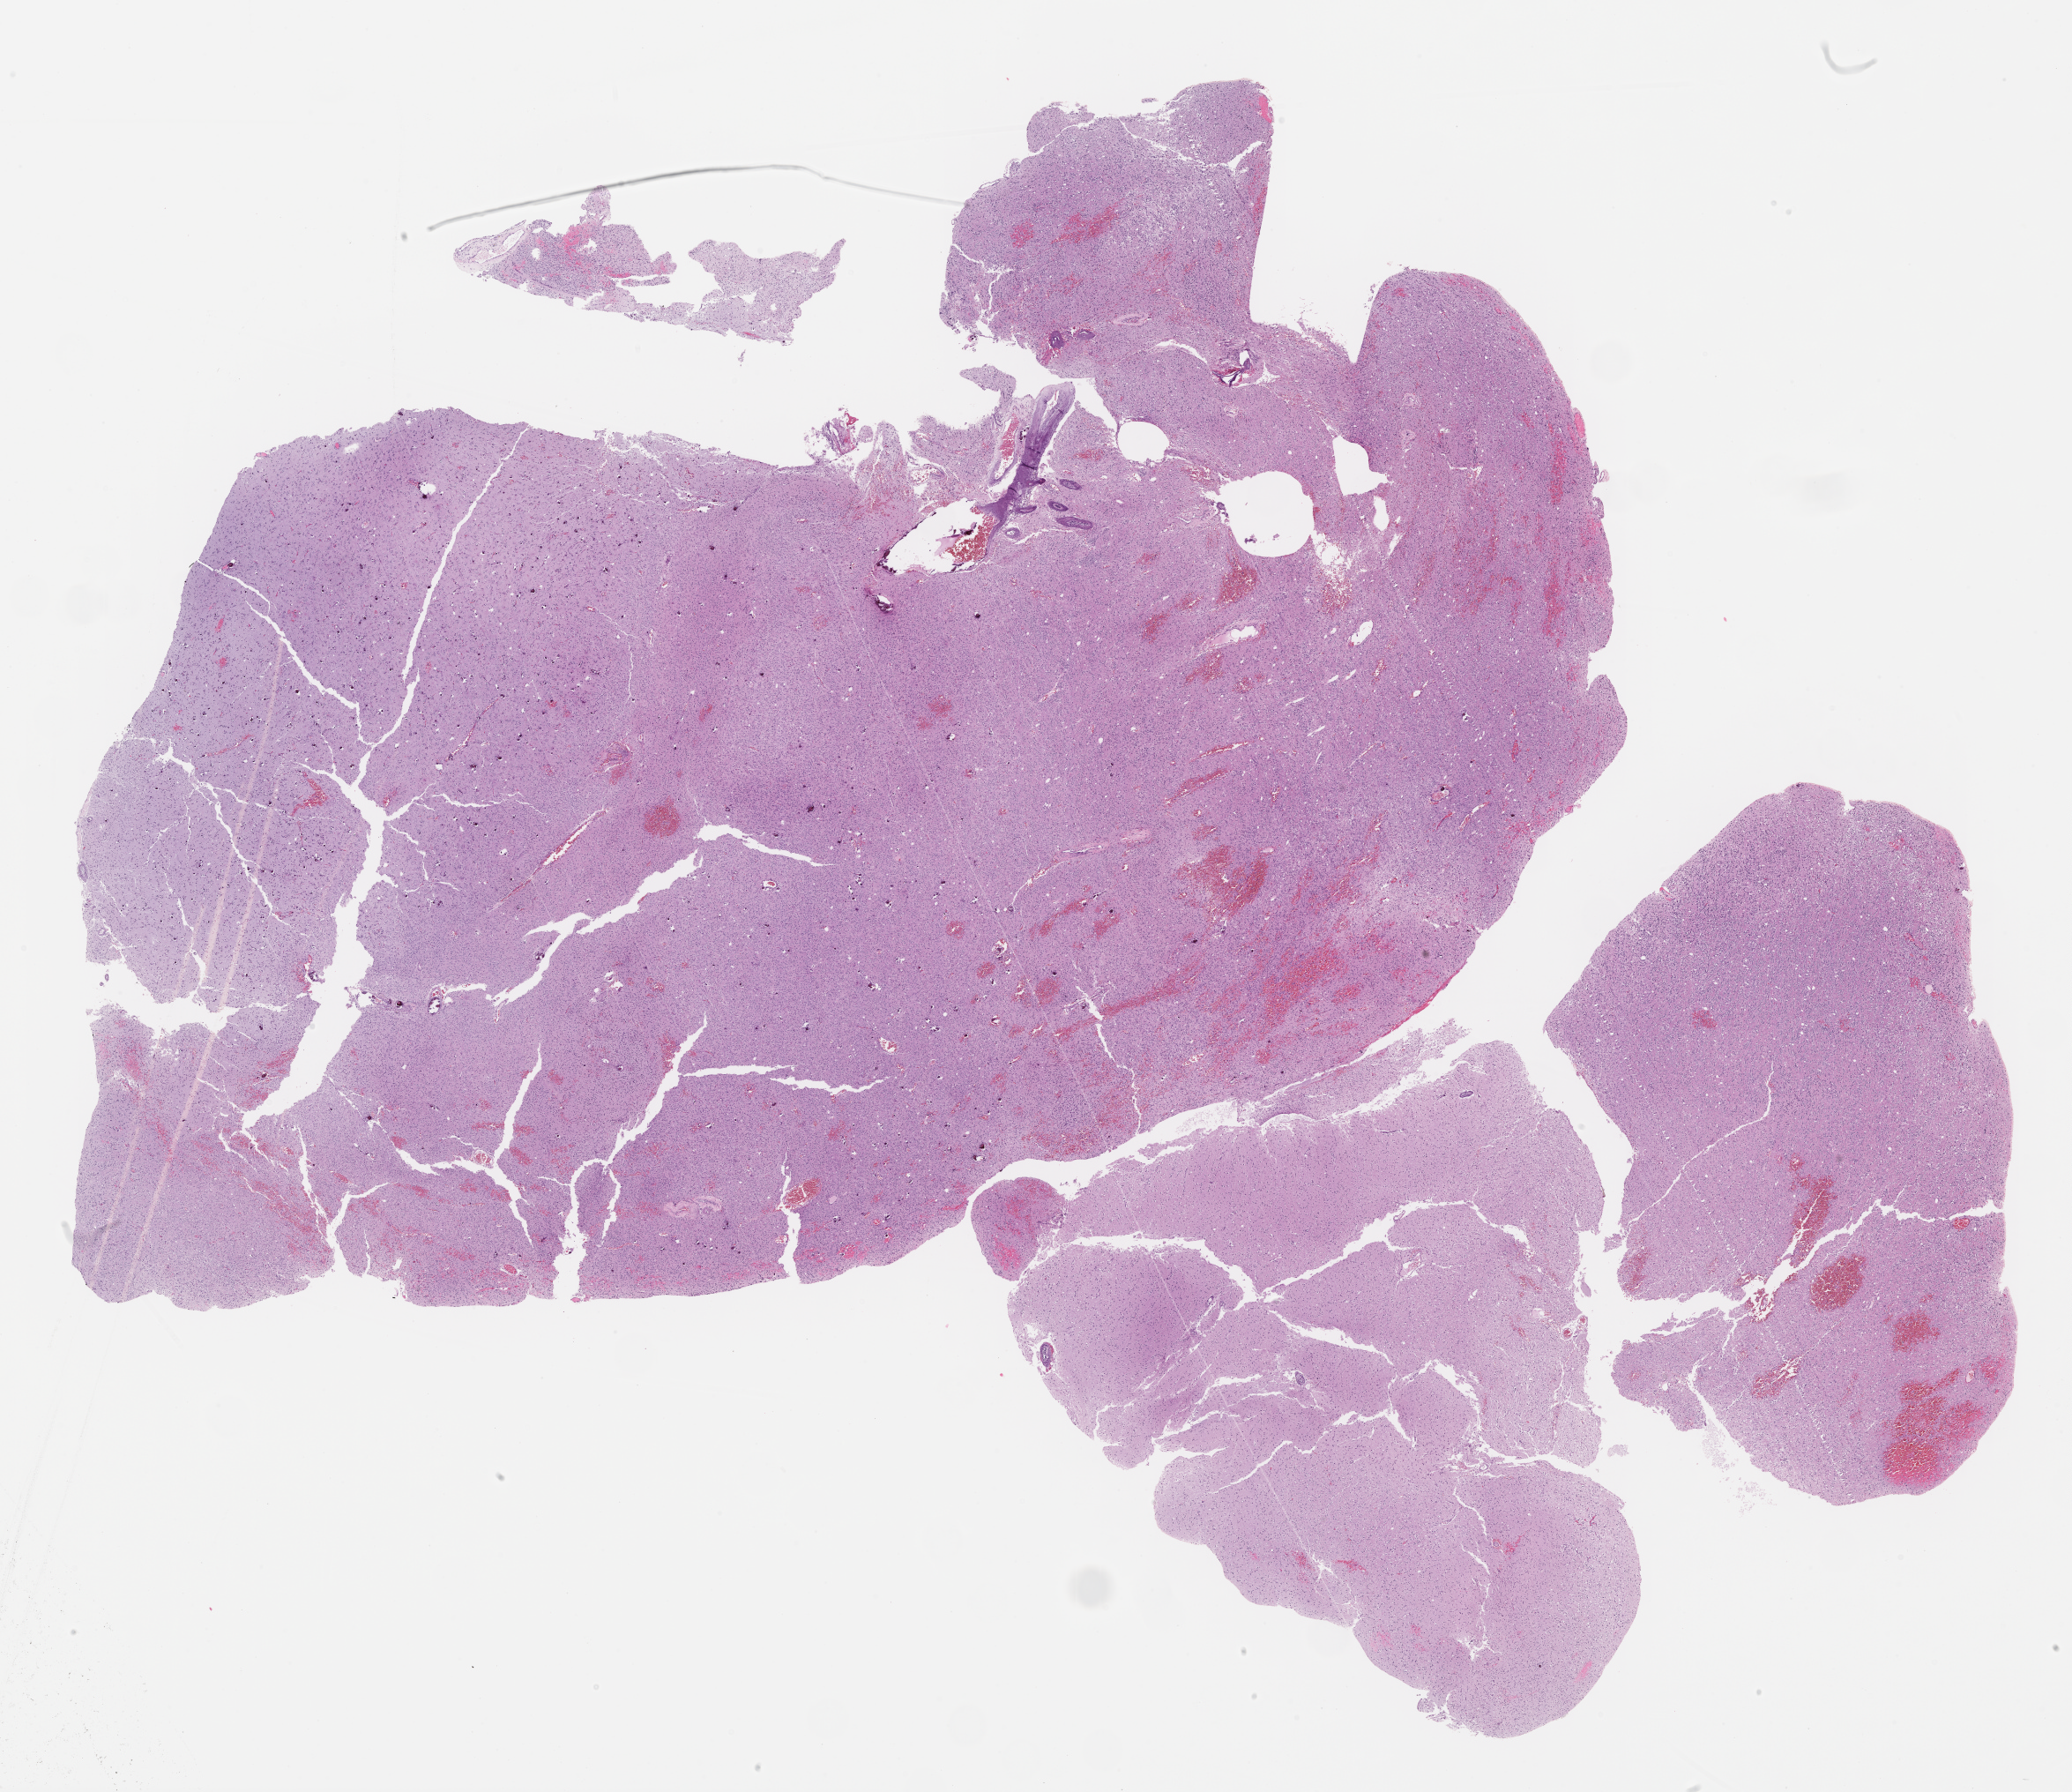
Whole-slide histology image, Hematoxylin and eosin (H&E) stained — whole scanned area (about 18.9 x 16.4 mm, from a 40x scan) shown as a low-resolution overview, formalin-fixed paraffin-embedded (FFPE) diagnostic section, sample: primary tumour, brain. Female patient; age at initial diagnosis 53 years. Histologic grade: G2 (moderately differentiated).
Laterality: right. Diagnosis: Oligodendroglioma, NOS (cerebrum).